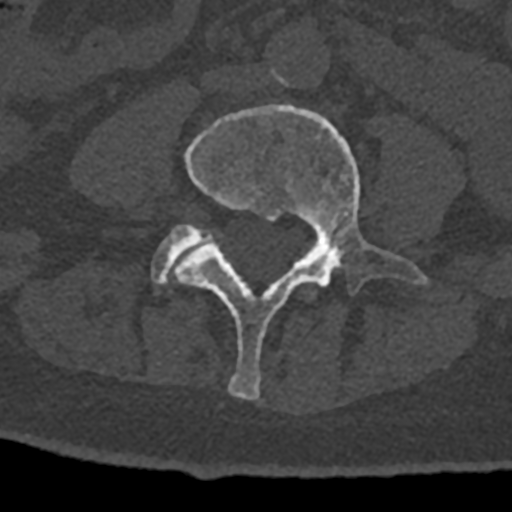
CT including the spine, one axial slice; slice 251 of 797 in the series (ordered by position); reconstruction kernel Br40s/3; 120 kVp; bone window (W 1800 / L 400 HU); 0.5 mm slice thickness; 512 × 512 image matrix. Patient: male, 74 years. Case-level facts recorded for this patient, not image findings: primary cancer: renal; vertebrae with lytic lesions (as recorded): T10, L1, L2, L3, L4, L5.
Structures marked on this image (semi-automatically segmented with operator editing):
- L4 vertebra: bounding box (x1, y1, x2, y2) in pixels: (174, 105, 428, 400)
- L5 vertebra: (151, 224, 213, 284)